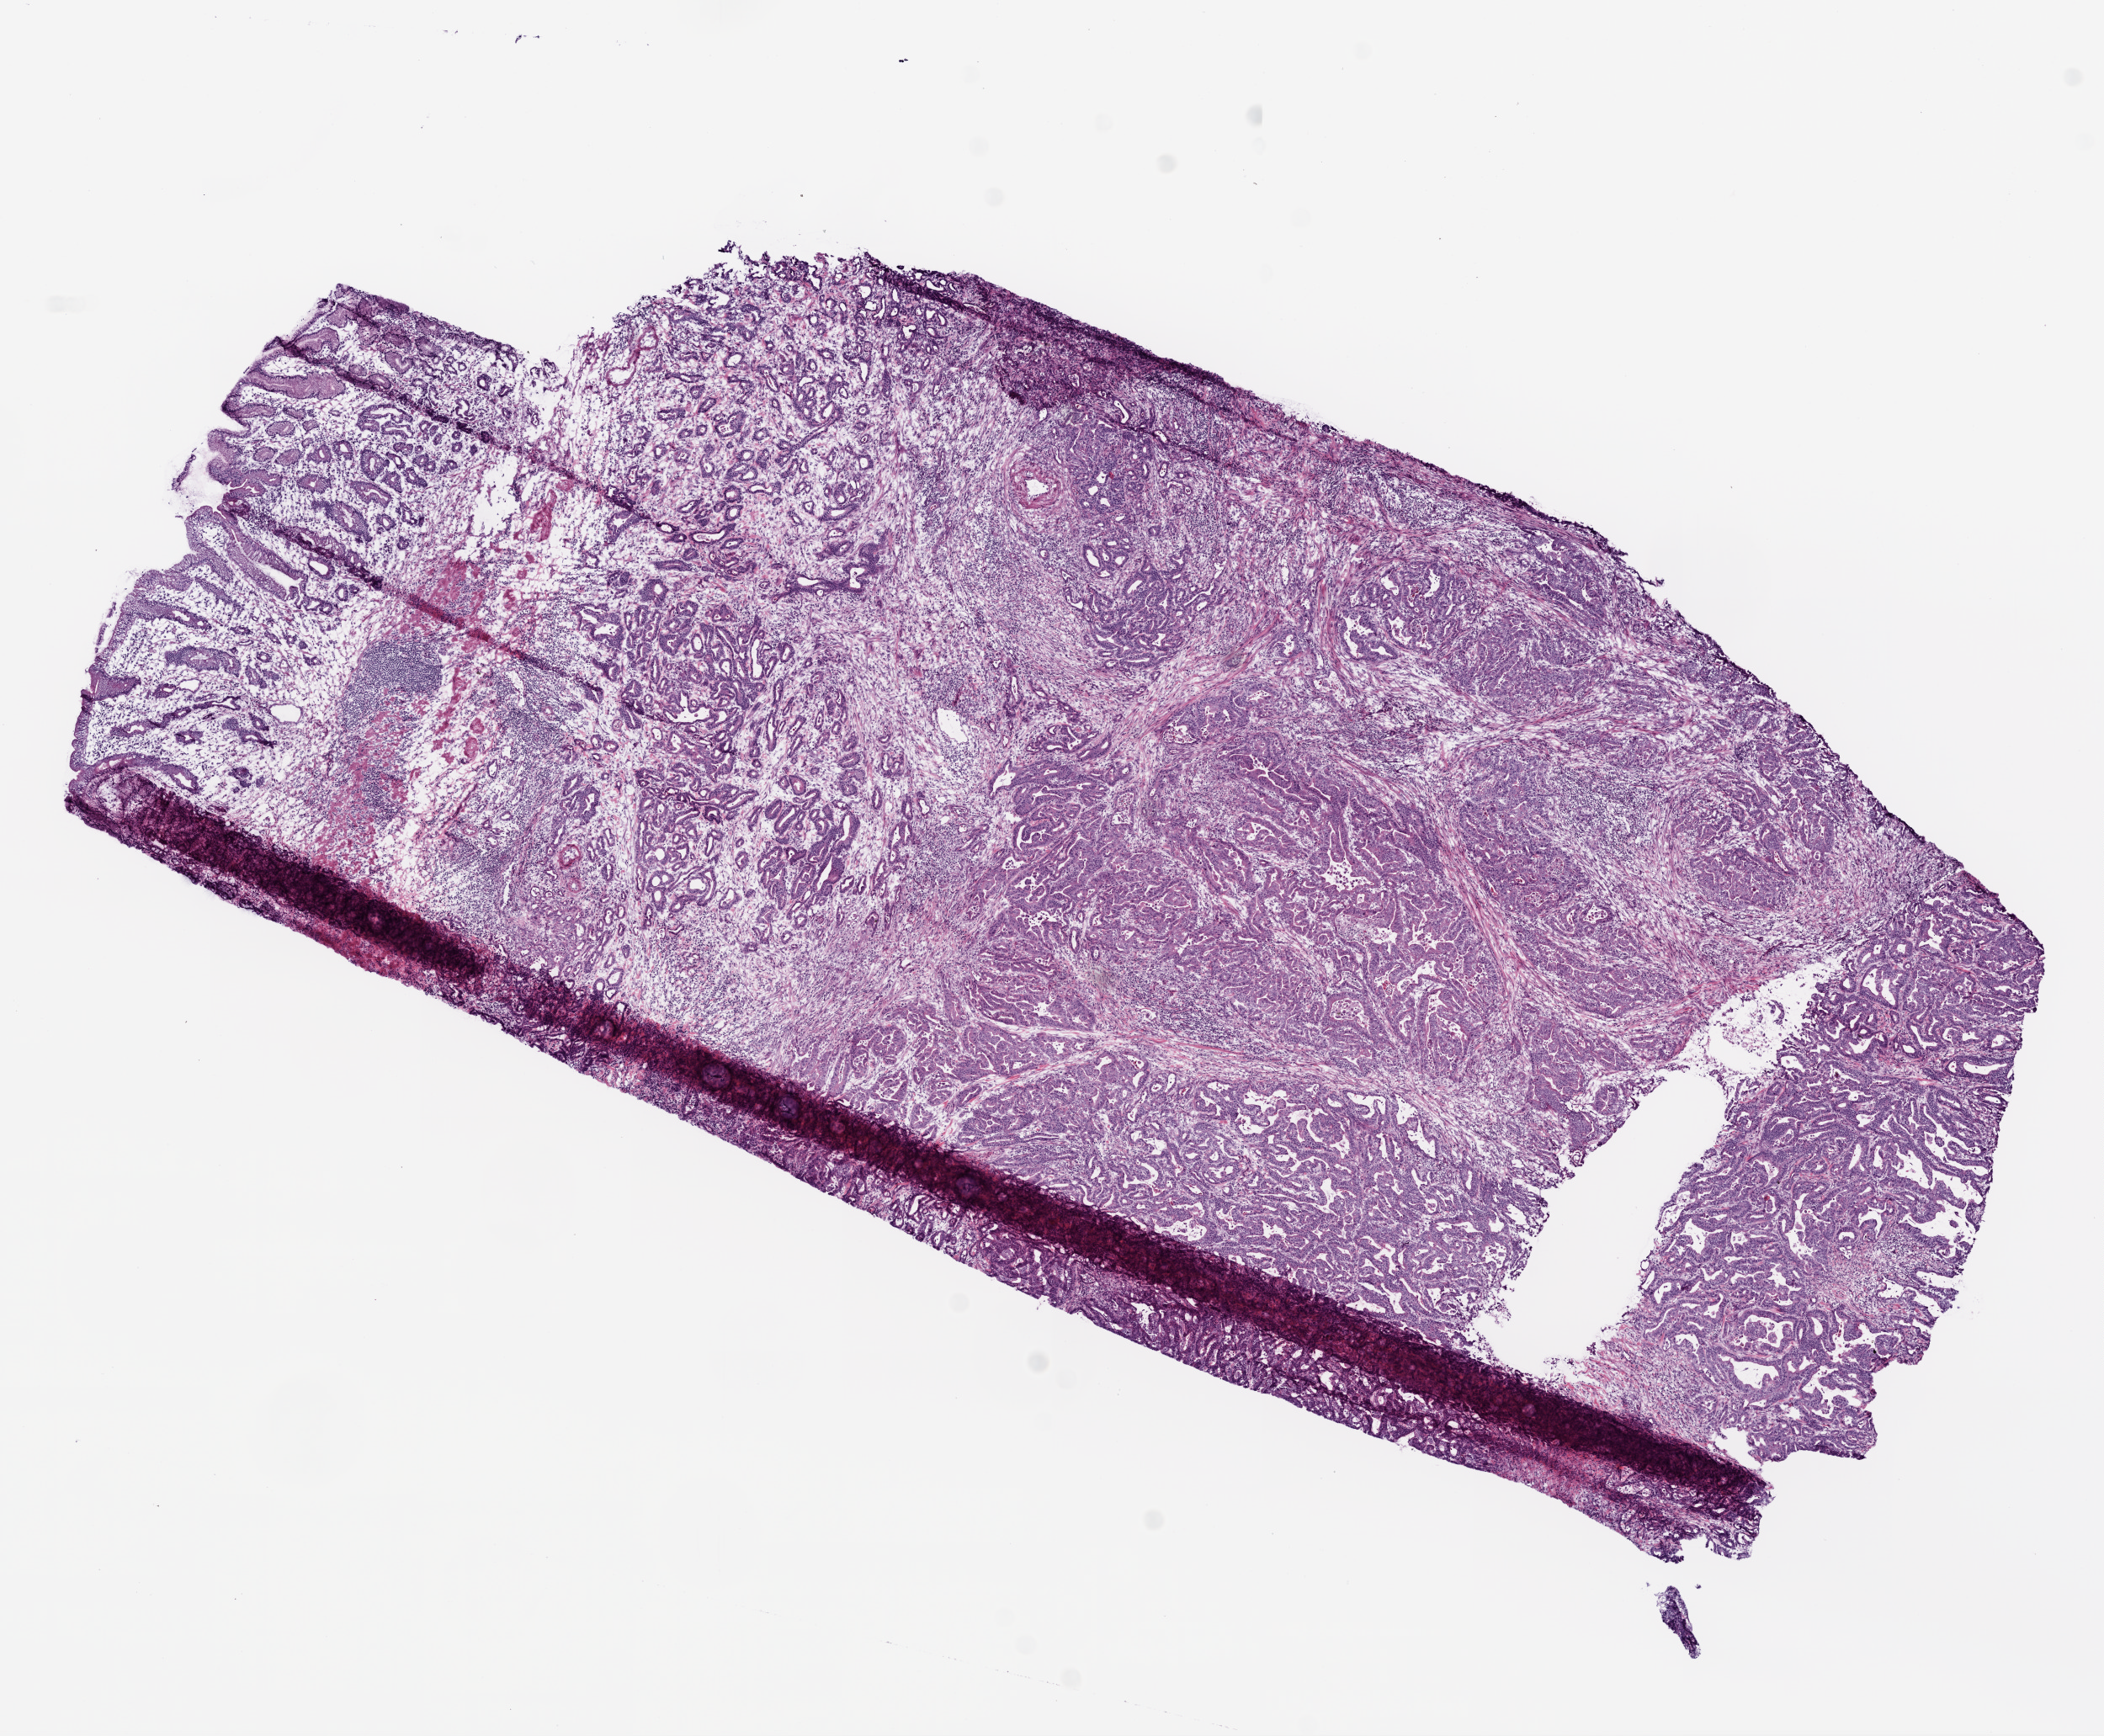
Digitized H&E tissue section (whole slide), a low-resolution overview of the entire scanned area, about 10.0 x 8.3 mm (slide scanned at 20x), frozen section from the bottom of the tissue portion, stomach, primary tumour sample. Patient: male, age at initial diagnosis 69 years. Histologic grade: G3 (poorly differentiated). Pathologist review of this section (percent, as recorded): tumour cells 80%, tumour nuclei 80%, normal cells 10%, stromal cells 10%, necrosis 0%. Infiltration values recorded for this section: lymphocyte infiltration 10%, monocyte infiltration 0%, neutrophil infiltration 5%.
Lymph nodes positive (case pathology): 2 of 41 examined. Histologic diagnosis: Adenocarcinoma, NOS (gastric antrum). AJCC pathologic stage: II.